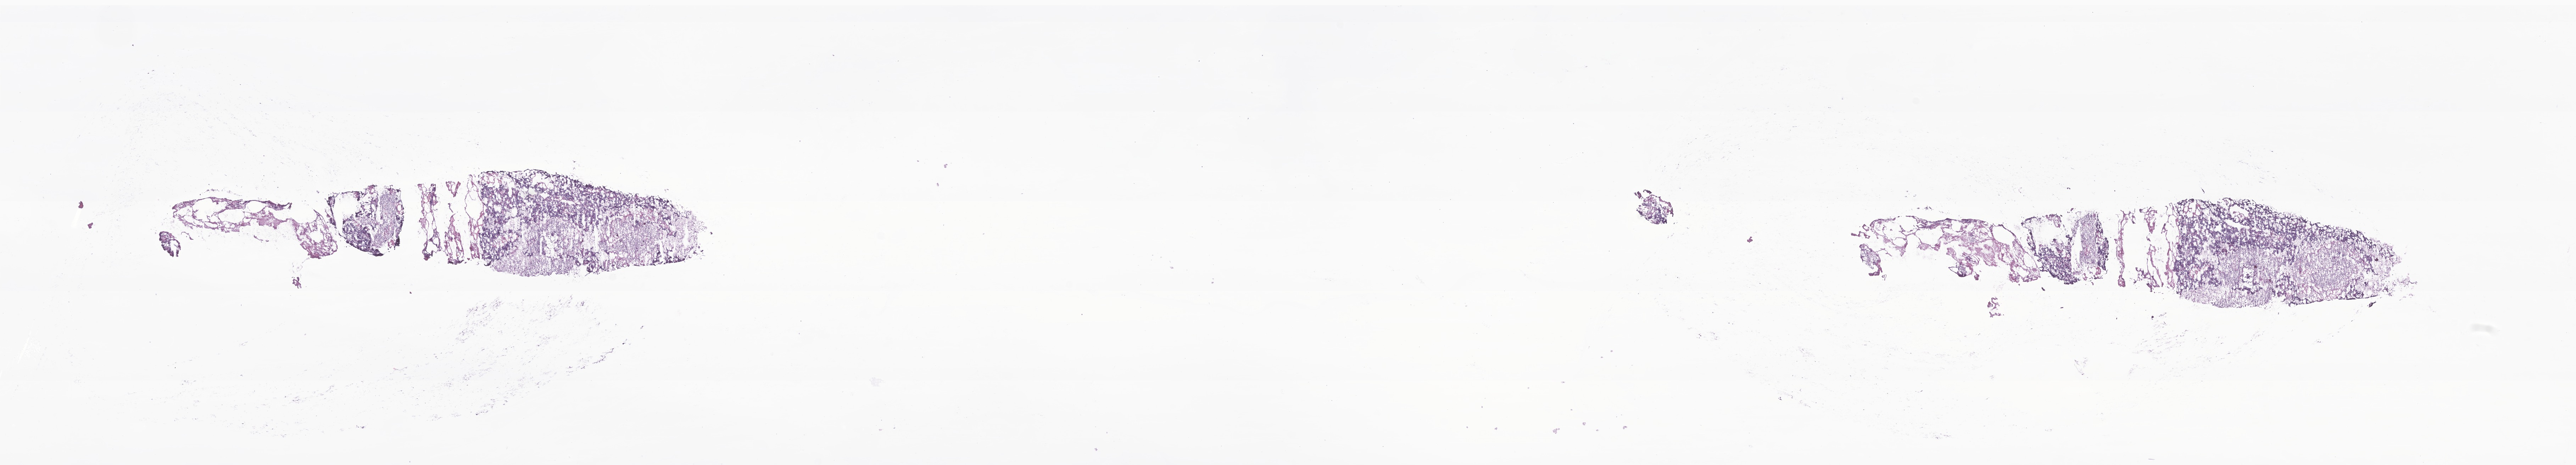
Digitized hematoxylin and eosin (H&E)-stained section of tumor tissue from the brain — whole scanned area (about 30.6 x 5.5 mm) shown as a low-resolution overview. Cryosection (OCT / tissue freezing medium). Patient male; age 77 months (6 years 5 months).
Recorded diagnosis: Medulloblastoma, NOS.